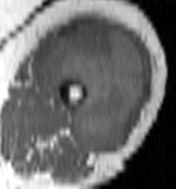
MRI of an extremity soft-tissue mass, one axial slice. Position 62 of 100 along the scan axis. MR volume resampled by the dataset authors to the PET/CT grid (not the native acquisition matrix). 176 × 189 image matrix, field of view 172 × 185 mm. Female patient. From the clinical record (not read from this slice): histological type: undifferentiated – high grade; grade: high; site of the primary tumour: left thigh.
Structures marked on this image (expert contour drawn on MRI and transferred to this co-registered scan by the dataset authors):
- gross tumour volume including surrounding oedema: bounding box <46,23,145,154> (left, top, right, bottom; pixels)
- gross tumour volume (mass): <46,23,143,154>